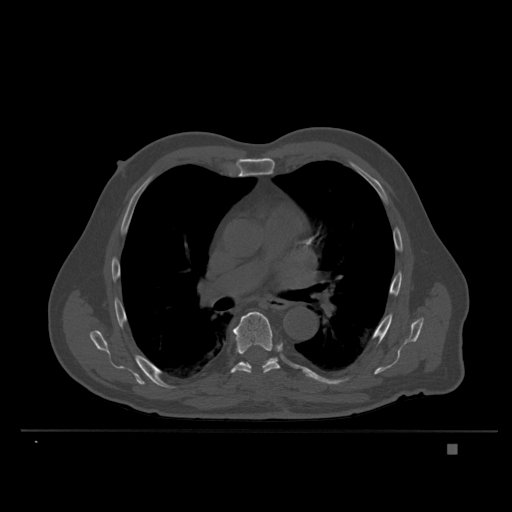
CT including the spine, one axial slice. Position 244 of 435 along the scan axis. Bone window (W 1800 / L 400 HU). 512 × 512 image matrix, field of view 434 × 434 mm. Patient: male, 73 years. Case-level facts recorded for this patient, not image findings: primary cancer: skin.
Annotated regions visible in this slice (semi-automatically segmented with operator editing):
- T7 vertebra: bounding box <231,312,280,374> (left, top, right, bottom; pixels)
- T8 vertebra: <241,358,278,363>